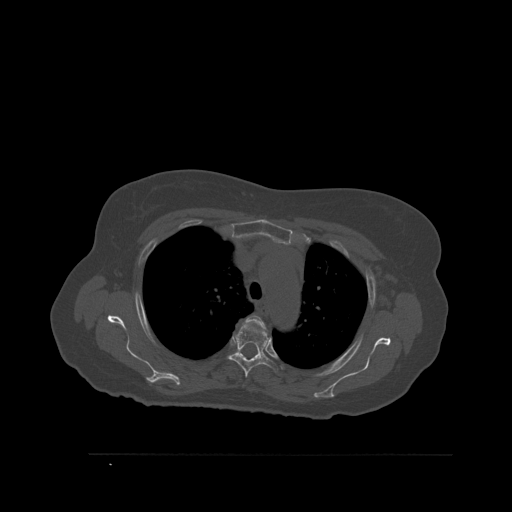
CT including the spine, one axial slice; position 409 of 527 along the scan axis; bone window (W 1800 / L 400 HU); 1.5 mm slice thickness; 512 × 512 image matrix. Patient: female, 73 years. Case-level facts recorded for this patient, not image findings: primary cancer: breast.
Outlined on this slice (semi-automatically segmented with operator editing):
- T3 vertebra: bounding box <242,315,265,327> (left, top, right, bottom; pixels)
- T4 vertebra: <228,324,278,378>